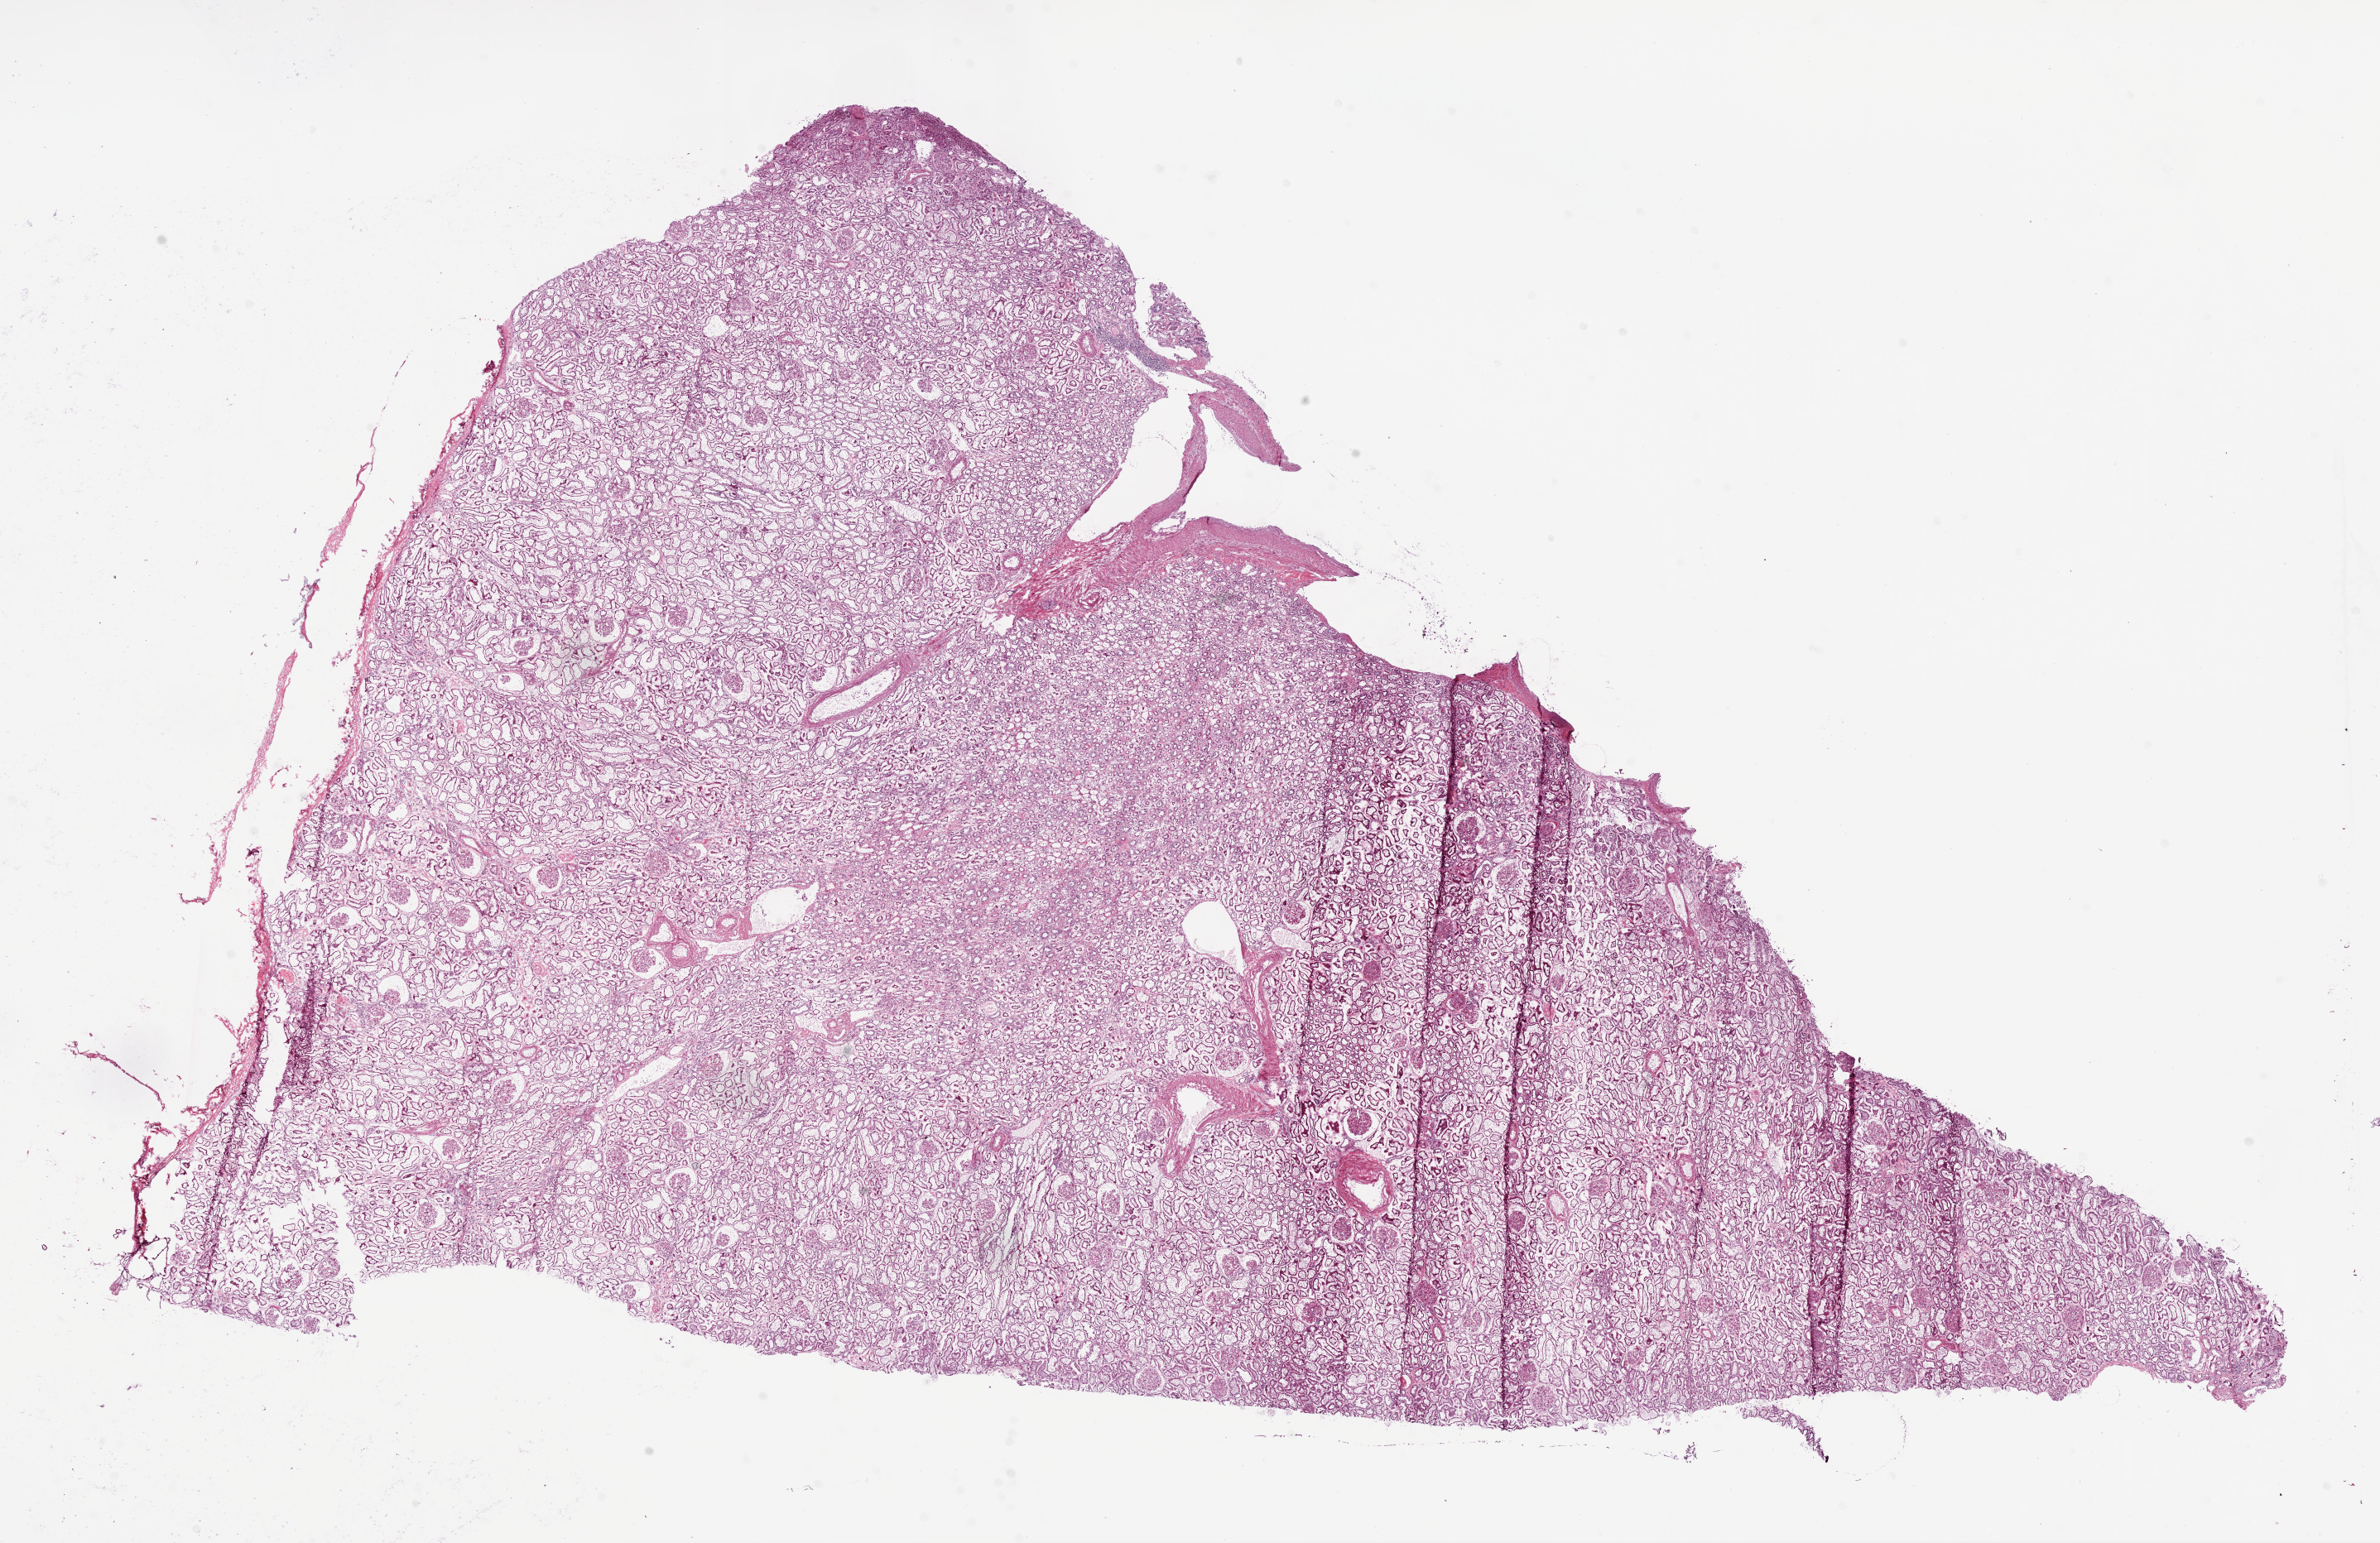
Digitized H&E-stained tissue section (whole slide) — a low-resolution overview of the entire scanned area, about 23.1 x 15.0 mm (from a 20x scan), frozen section from the bottom of the tissue portion, solid tissue normal (non-tumour tissue) sample from the kidney. Female patient; age at initial diagnosis 69 years.
This section: solid tissue normal sample (biorepository sample class). Patient diagnosis: Clear cell adenocarcinoma, NOS.